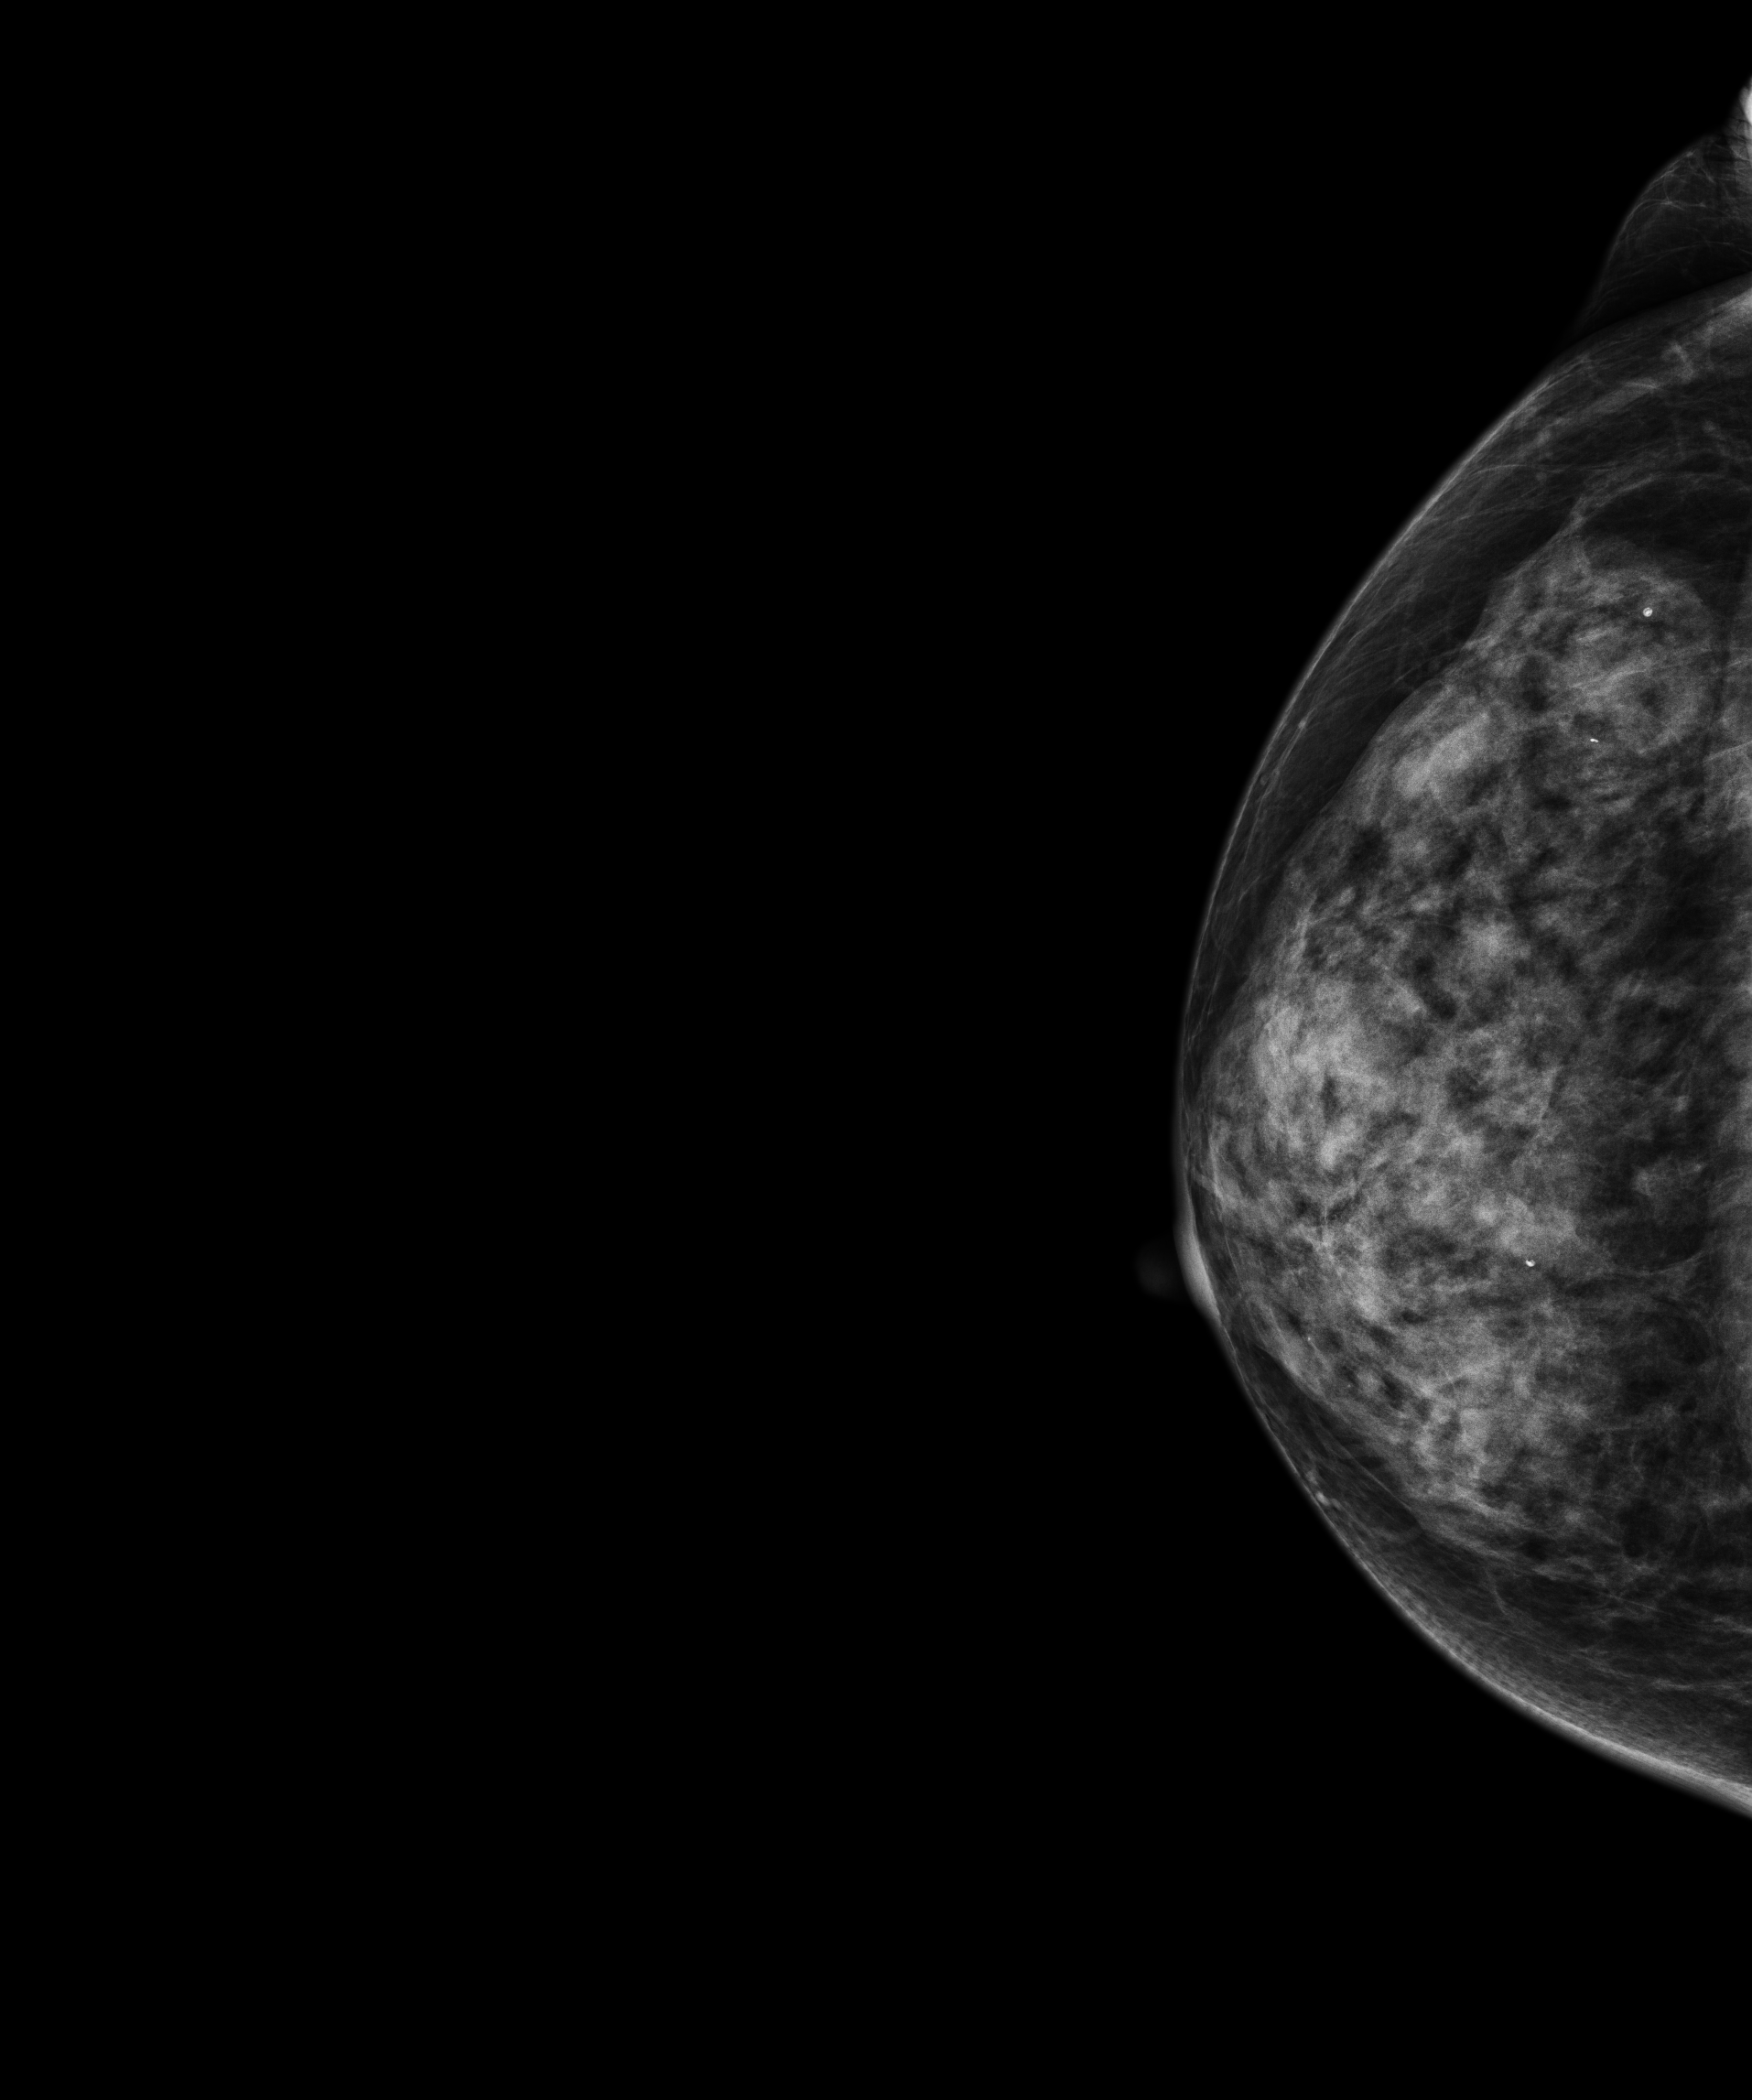
Digital mammogram (FFDM); right breast; CC view; screening examination; compressed breast thickness 44 mm; system: Senographe Essential ADS_56.21.3. Patient: female, 67 years.
BI-RADS breast density category at the screening exam (both breasts, scale 1–4): 3. Final BI-RADS assessment for this screening round (tomosynthesis exam, both breasts): category 1. Recall: no recall after this screen.